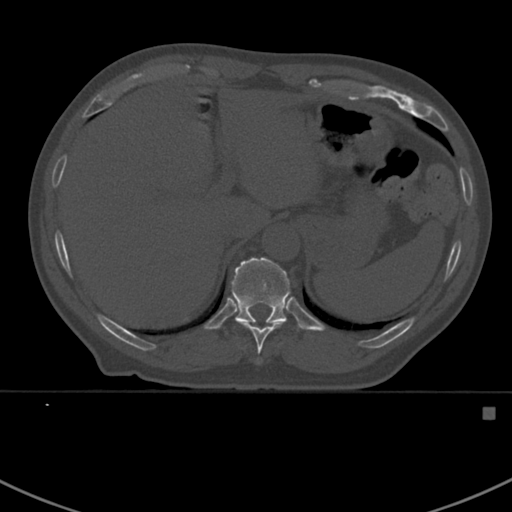
CT including the spine, one axial slice; slice 357 of 412 in the series (ordered by position); reconstruction kernel Br40s; 120 kVp; bone window (W 1800 / L 400 HU); 1.5 mm slice thickness; 512 × 512 image matrix, field of view 358 × 358 mm. Patient: male, 59 years. From the clinical record (not read from this slice): primary cancer: prostate.
Annotated regions visible in this slice (semi-automatically segmented with operator editing):
- T10 vertebra: bounding box [x1, y1, x2, y2] px = [237, 322, 284, 364]
- T11 vertebra: [231, 257, 302, 331]